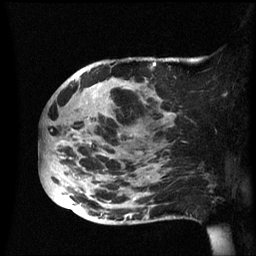
Breast MRI (dynamic contrast-enhanced), one sagittal slice; position 23 of 60 along the scan axis; dynamic contrast-enhanced series, image 2 of 3 at this slice position (ordered by acquisition); 1.5 T; TE 4.2 ms, TR 8.4 ms; 2.4 mm slice thickness; 256 × 256 image matrix, field of view 230 × 230 mm. Female patient, age 49 years.
Annotated regions visible in this slice (semi-automatically segmented with operator editing):
- analysis volume of interest (the breast-tissue region the enhancement analysis was run in; not a lesion): bounding box <40,57,174,225> (left, top, right, bottom; pixels)
- tumour enhancement mask (voxels above the 70 % enhancement threshold inside the analysis volume of interest): <153,62,171,115>